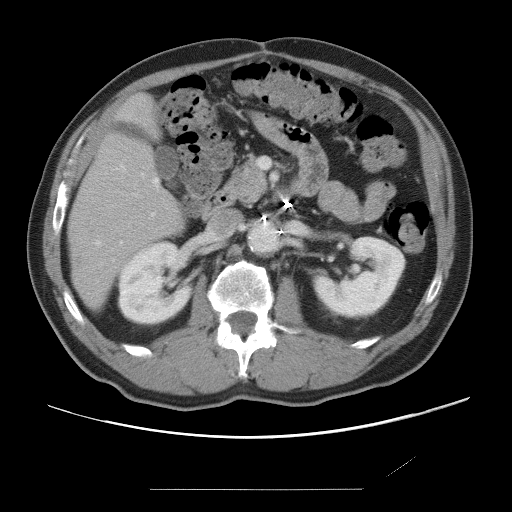
Contrast-enhanced abdominal CT, one axial slice; position 30 of 87 along the scan axis; intravenous contrast given; soft-tissue window (W 400 / L 40 HU); 5 mm slice thickness; 512 × 512 image matrix. Male patient, age 74 years. Case-level facts recorded for this patient, not image findings: diagnosis: colorectal cancer liver metastases, imaged before liver resection; multiple liver metastases: yes; largest metastasis: 1.1 cm; disease in both lobes: no.
Annotated regions visible in this slice (manually delineated by an expert):
- hepatic veins: box from (x=96, y=166) to (x=158, y=244) px
- liver: (x=69, y=97)–(x=183, y=307)
- planned liver remnant (the part of the liver to remain after resection): (x=69, y=98)–(x=183, y=307)
- portal vein (with intrahepatic branches): (x=141, y=174)–(x=155, y=216)
- liver metastasis: (x=76, y=256)–(x=83, y=266)